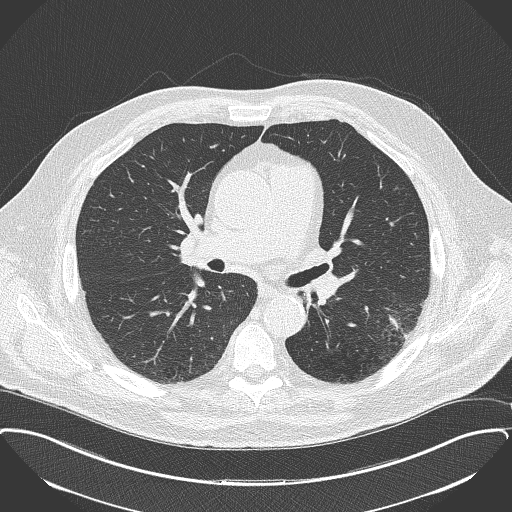
Chest CT (low-dose screening protocol), one axial image, second annual screen, lung window (W 1500 / L -600 HU), 2 mm slice thickness, 512 × 512 image matrix, field of view 400 × 400 mm. Male, age 68 years at enrolment. Former smoker at enrolment.
- Expert-annotated lung lesion, bounding box [x1, y1, x2, y2] px = [374, 294, 431, 346].
- The screening reader recorded 2 non-calcified nodules or masses ≥4 mm on this exam (left lower lobe, left lower lobe); which of them this box marks is not recorded.
- Official screen result: positive, other.